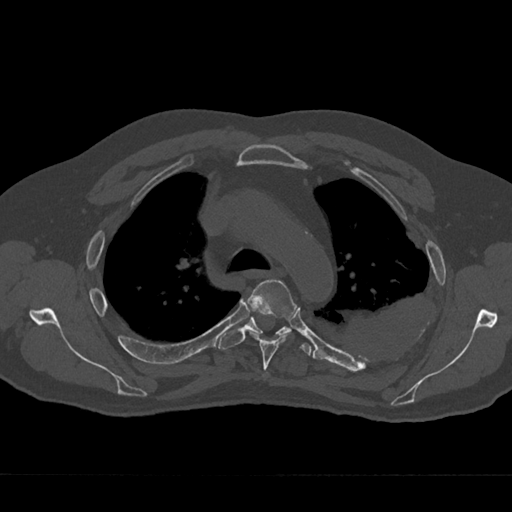
CT including the spine, one axial slice. Slice 502 of 797 in the series (ordered by position). Bone window (W 1800 / L 400 HU). 0.5 mm slice thickness. 512 × 512 image matrix. Patient: male, 75 years. From the clinical record (not read from this slice): primary cancer: renal.
Annotated regions visible in this slice (semi-automatic segmentation, software-assisted and operator-edited):
- T4 vertebra: bounding box [x1, y1, x2, y2] px = [245, 279, 295, 377]
- T5 vertebra: [219, 317, 312, 355]